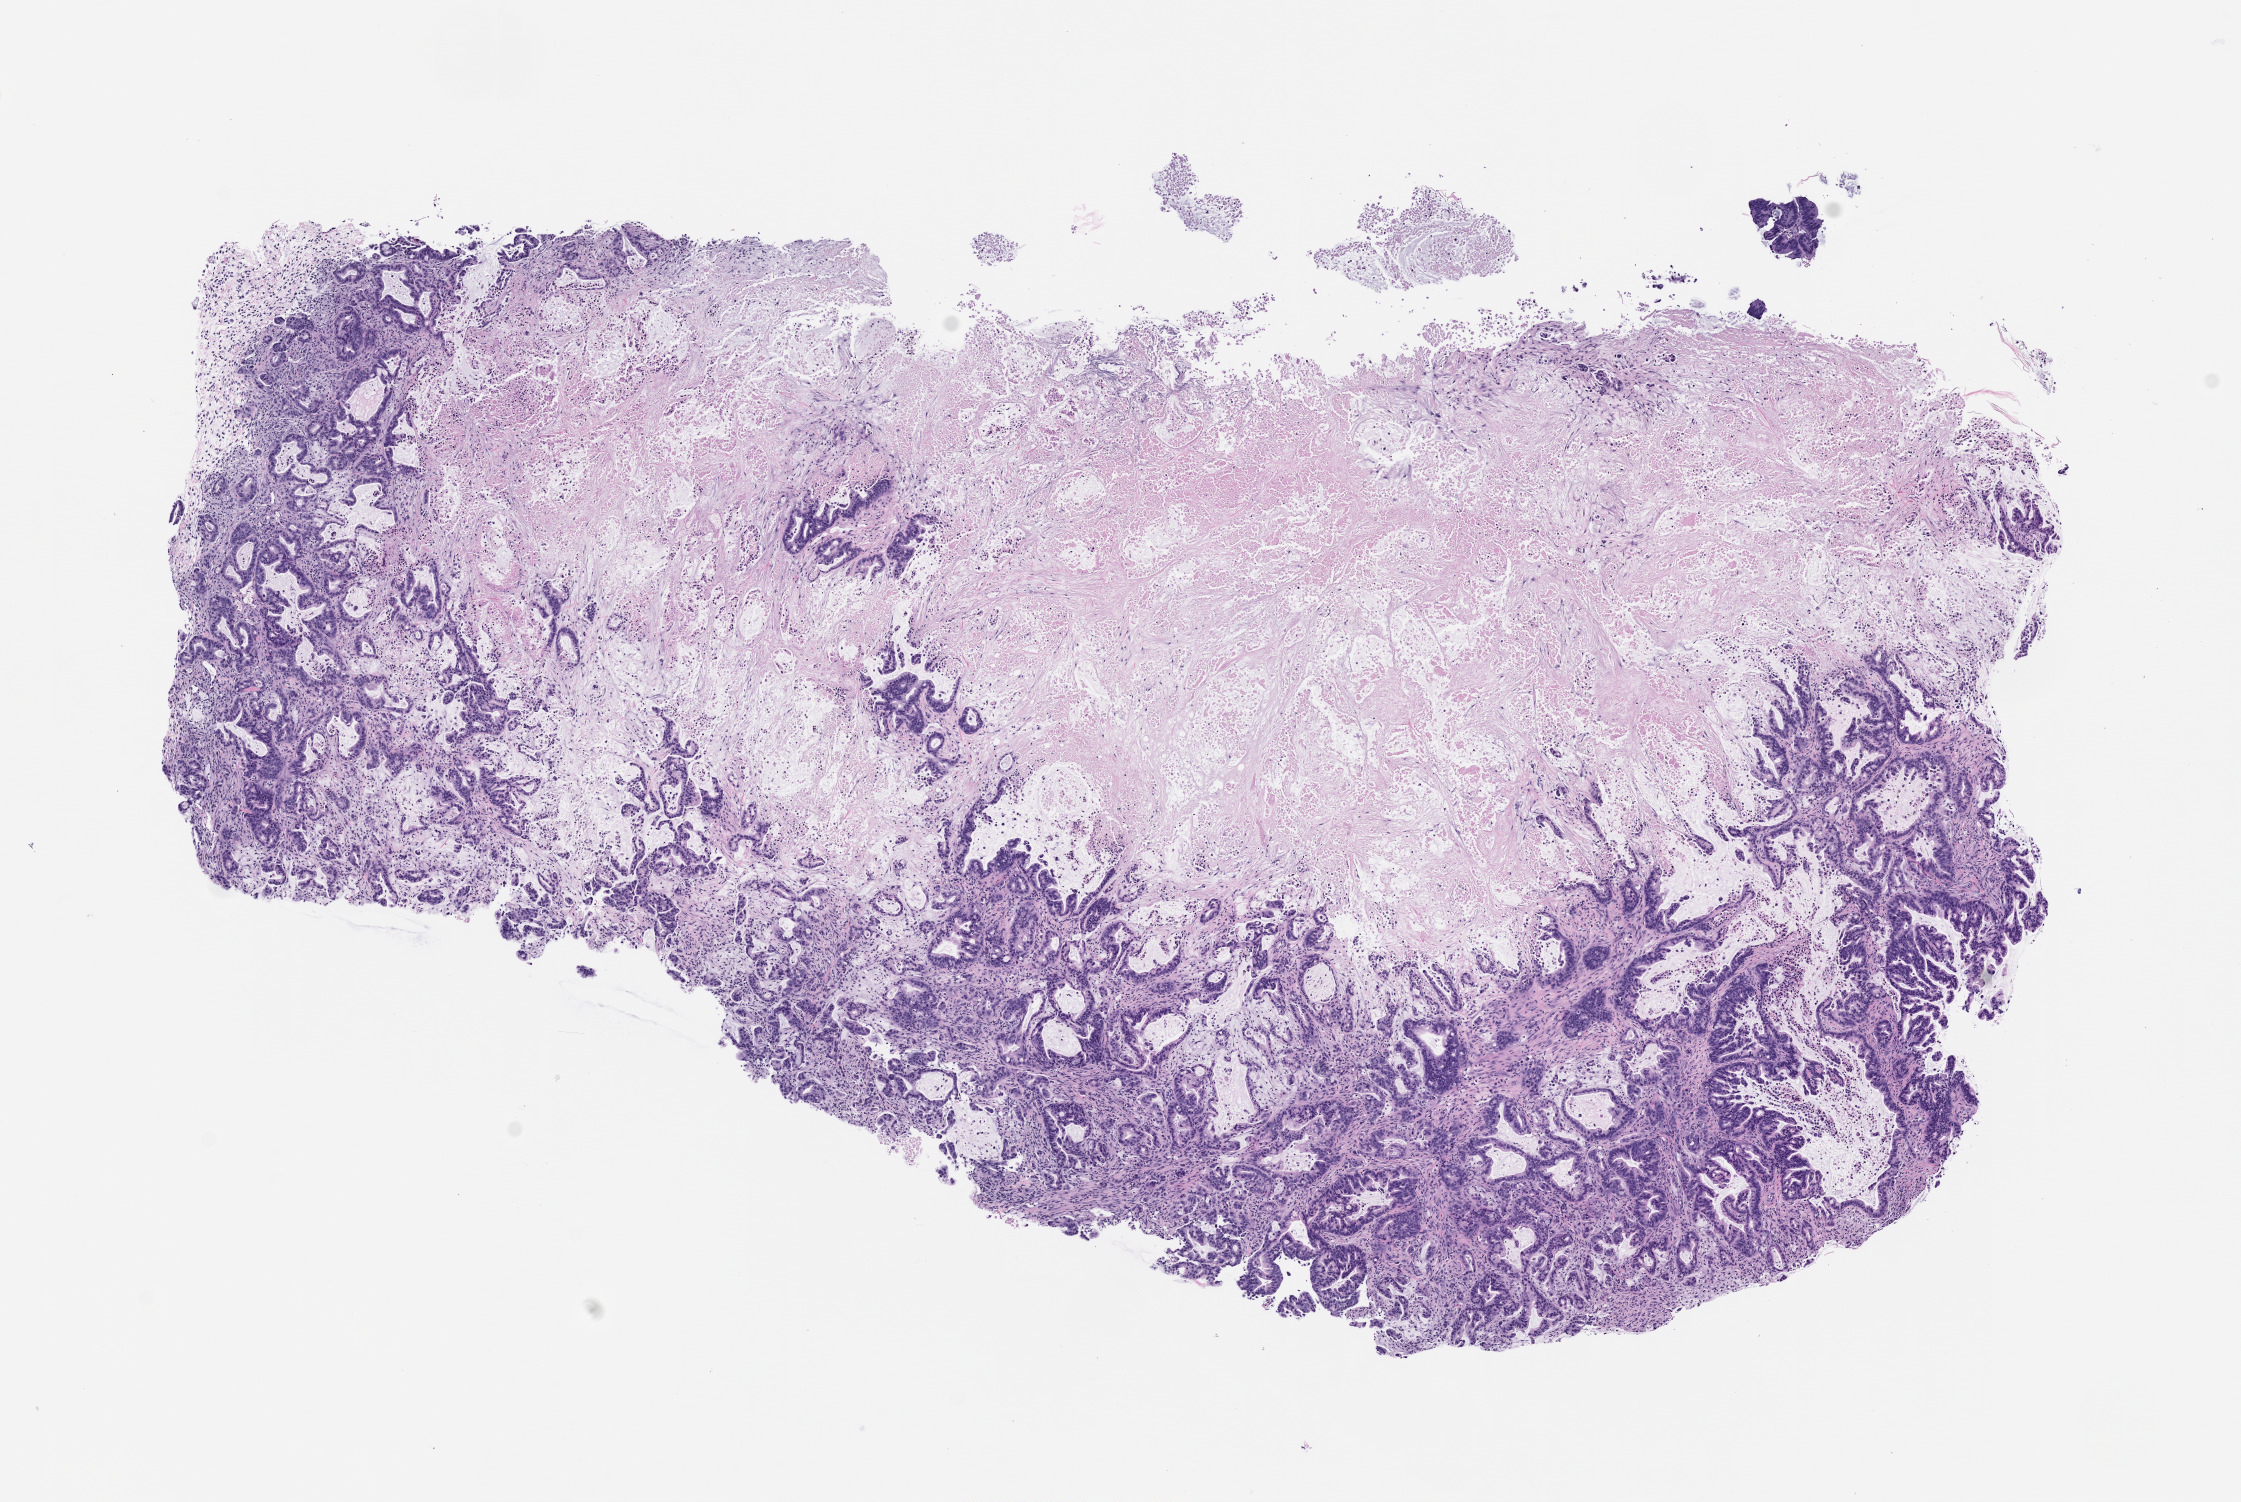
Whole-slide image, H&E: patient-derived xenograft (human tumor grown in a mouse), passage 3, a low-resolution overview of the entire scanned area, about 9.0 x 6.0 mm. Formalin-fixed paraffin-embedded section. Originating tumor site category: pancreas.
Originating patient diagnosis: Pancreatic Adenocarcinoma.